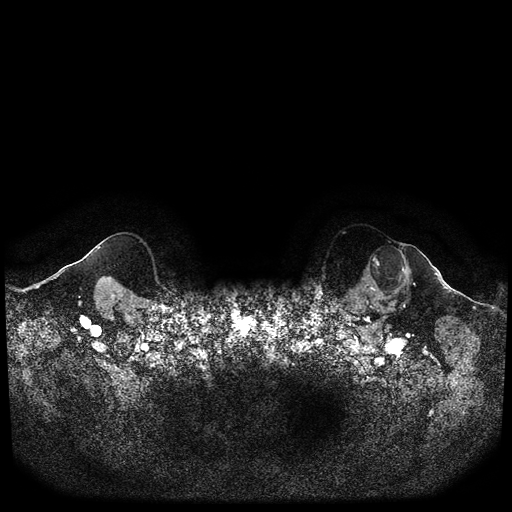
Breast MRI (dynamic contrast-enhanced, multi-phase), one axial slice; position 99 of 116 along the scan axis; dynamic contrast-enhanced series, time point 2 of 5 at this slice position (early post-contrast); 1.5 T; TE 2.6 ms, TR 5.3 ms; 2 mm slice thickness; 512 × 512 image matrix. Patient: female, 64 years.
Structures marked on this image (semi-automatic segmentation, software-assisted and operator-edited):
- breast lesion (labelled 'tumour' in the annotation; benign lesions carry a separate 'benign' label): bounding box <361,245,414,303> (left, top, right, bottom; pixels)